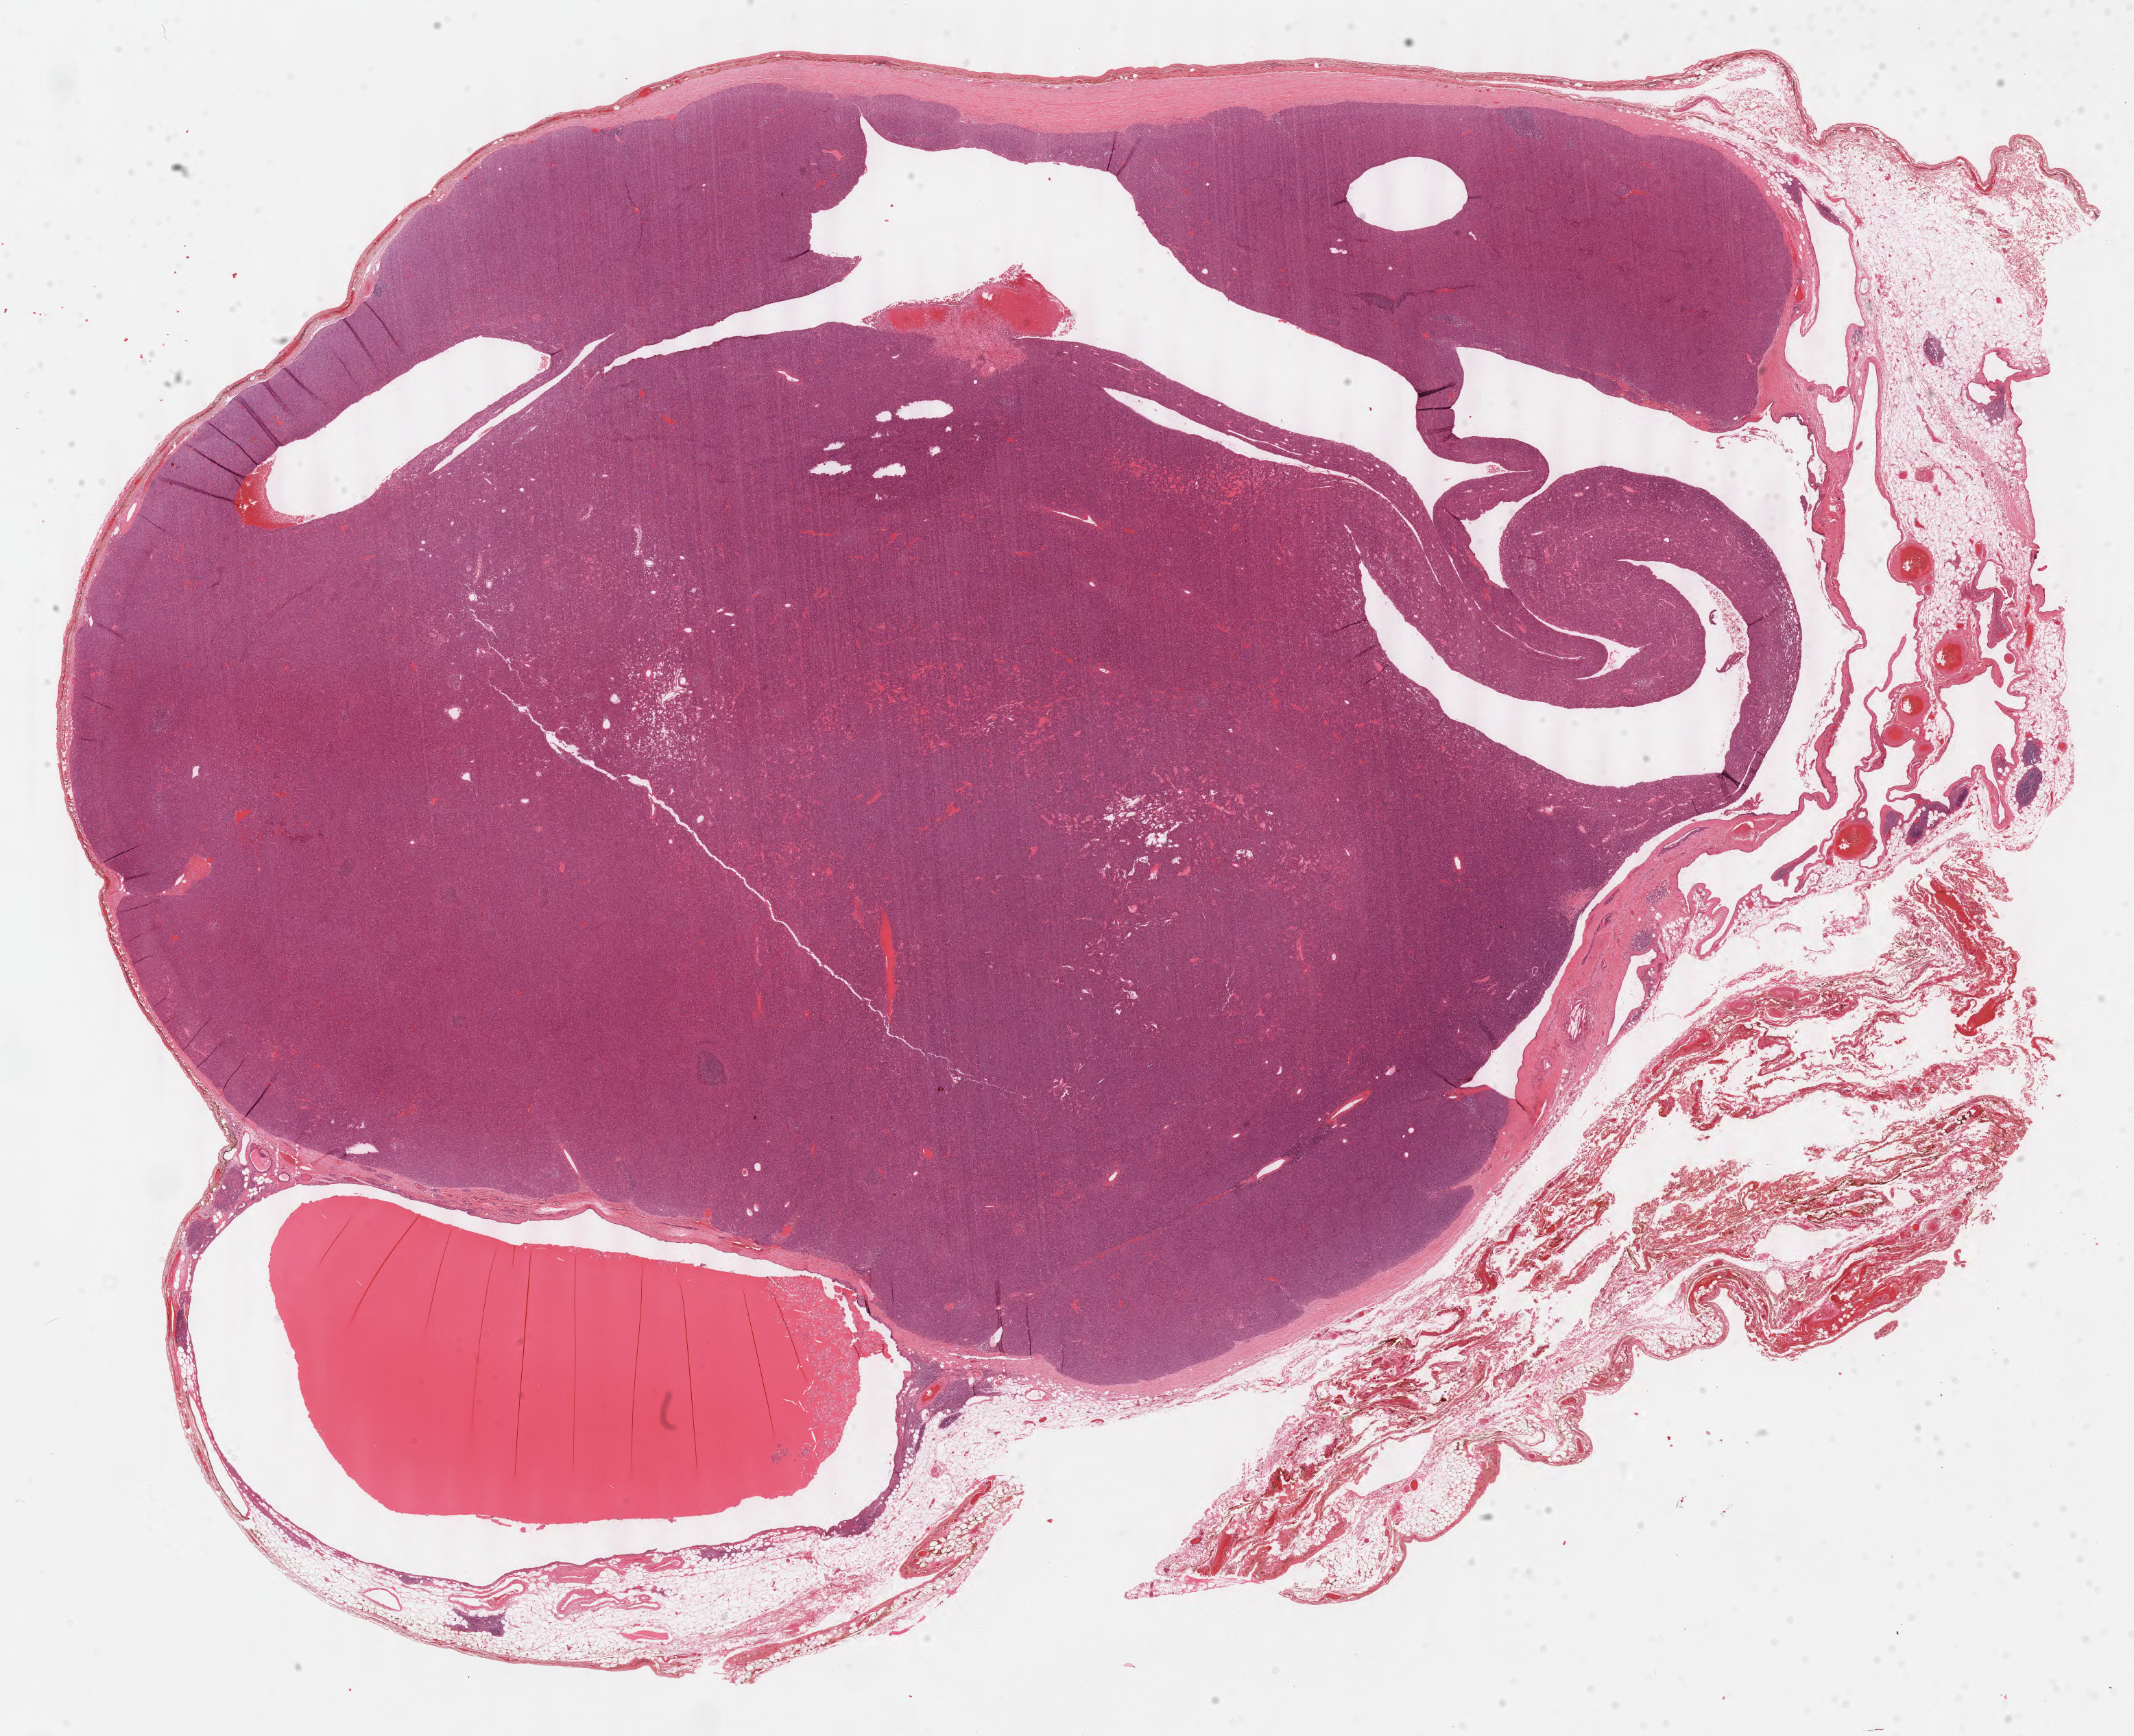
Whole-slide histology image, H&E-stained — a low-resolution overview of the entire scanned area, about 24.6 x 20.0 mm (slide scanned at 40x), formalin-fixed paraffin-embedded (FFPE) diagnostic section, thymus, primary tumour sample. Patient: male, age at initial diagnosis 63 years.
Diagnosis: Thymoma, type A, NOS.